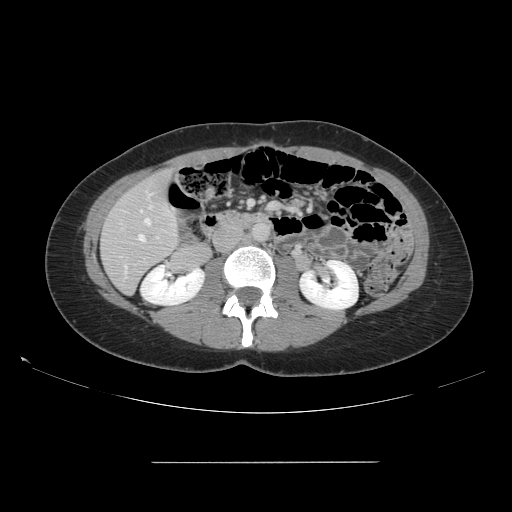
Contrast-enhanced abdominal CT, one axial slice. Position 55 of 151 along the scan axis. 120 kVp. Intravenous contrast given. Soft-tissue window (W 400 / L 40 HU). 2.5 mm slice thickness. 512 × 512 image matrix, field of view 421 × 421 mm. Female patient, age 46 years. From the clinical record (not read from this slice): diagnosis: colorectal cancer liver metastases, imaged before liver resection; multiple liver metastases: yes; largest metastasis: 3 cm; disease in both lobes: yes.
Structures marked on this image (outlined manually by an expert reader):
- hepatic veins: bounding box [x1, y1, x2, y2] px = [139, 211, 151, 242]
- liver: [102, 171, 178, 293]
- planned liver remnant (the part of the liver to remain after resection): [102, 171, 178, 293]
- portal vein (with intrahepatic branches): [156, 236, 159, 239]